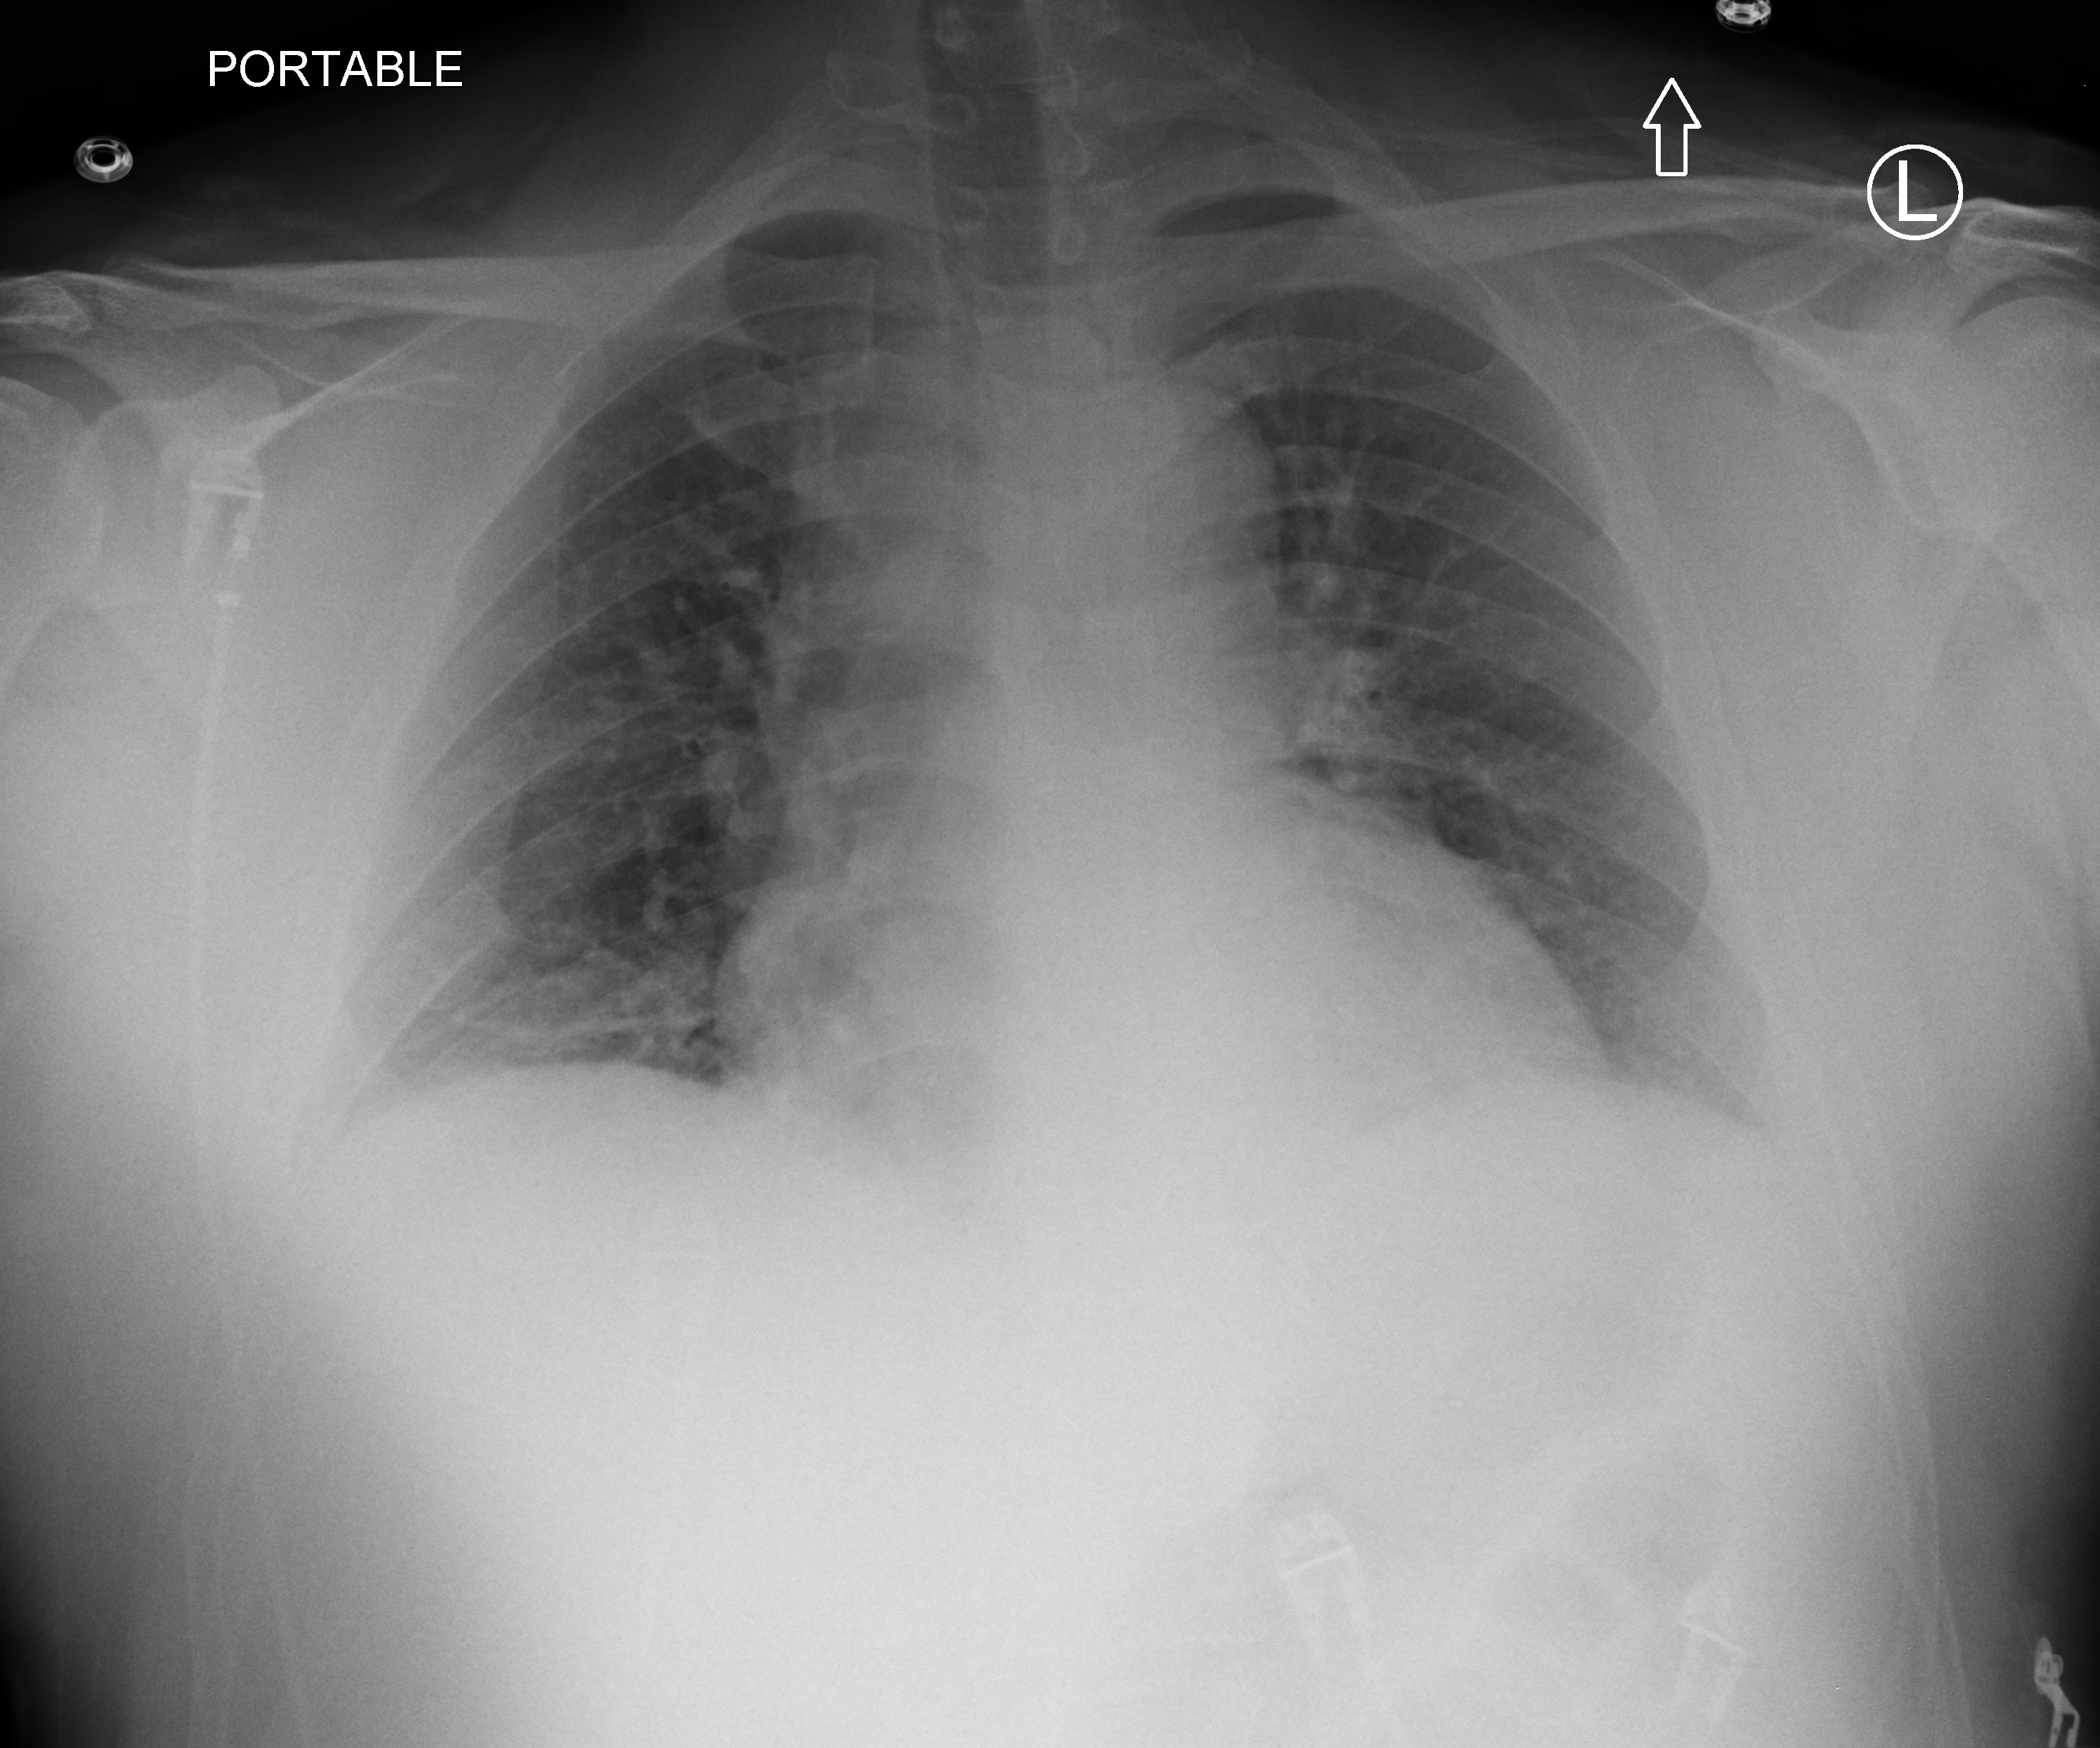
Portable chest radiograph, anteroposterior (AP) projection. Patient hospitalised with COVID-19; male, aged 18–59 years.
Hospital-stay facts (about this admission, not read from this image; timing relative to this image not recorded): admitted to intensive care during this hospital stay: no; mechanically ventilated during this hospital stay: no.